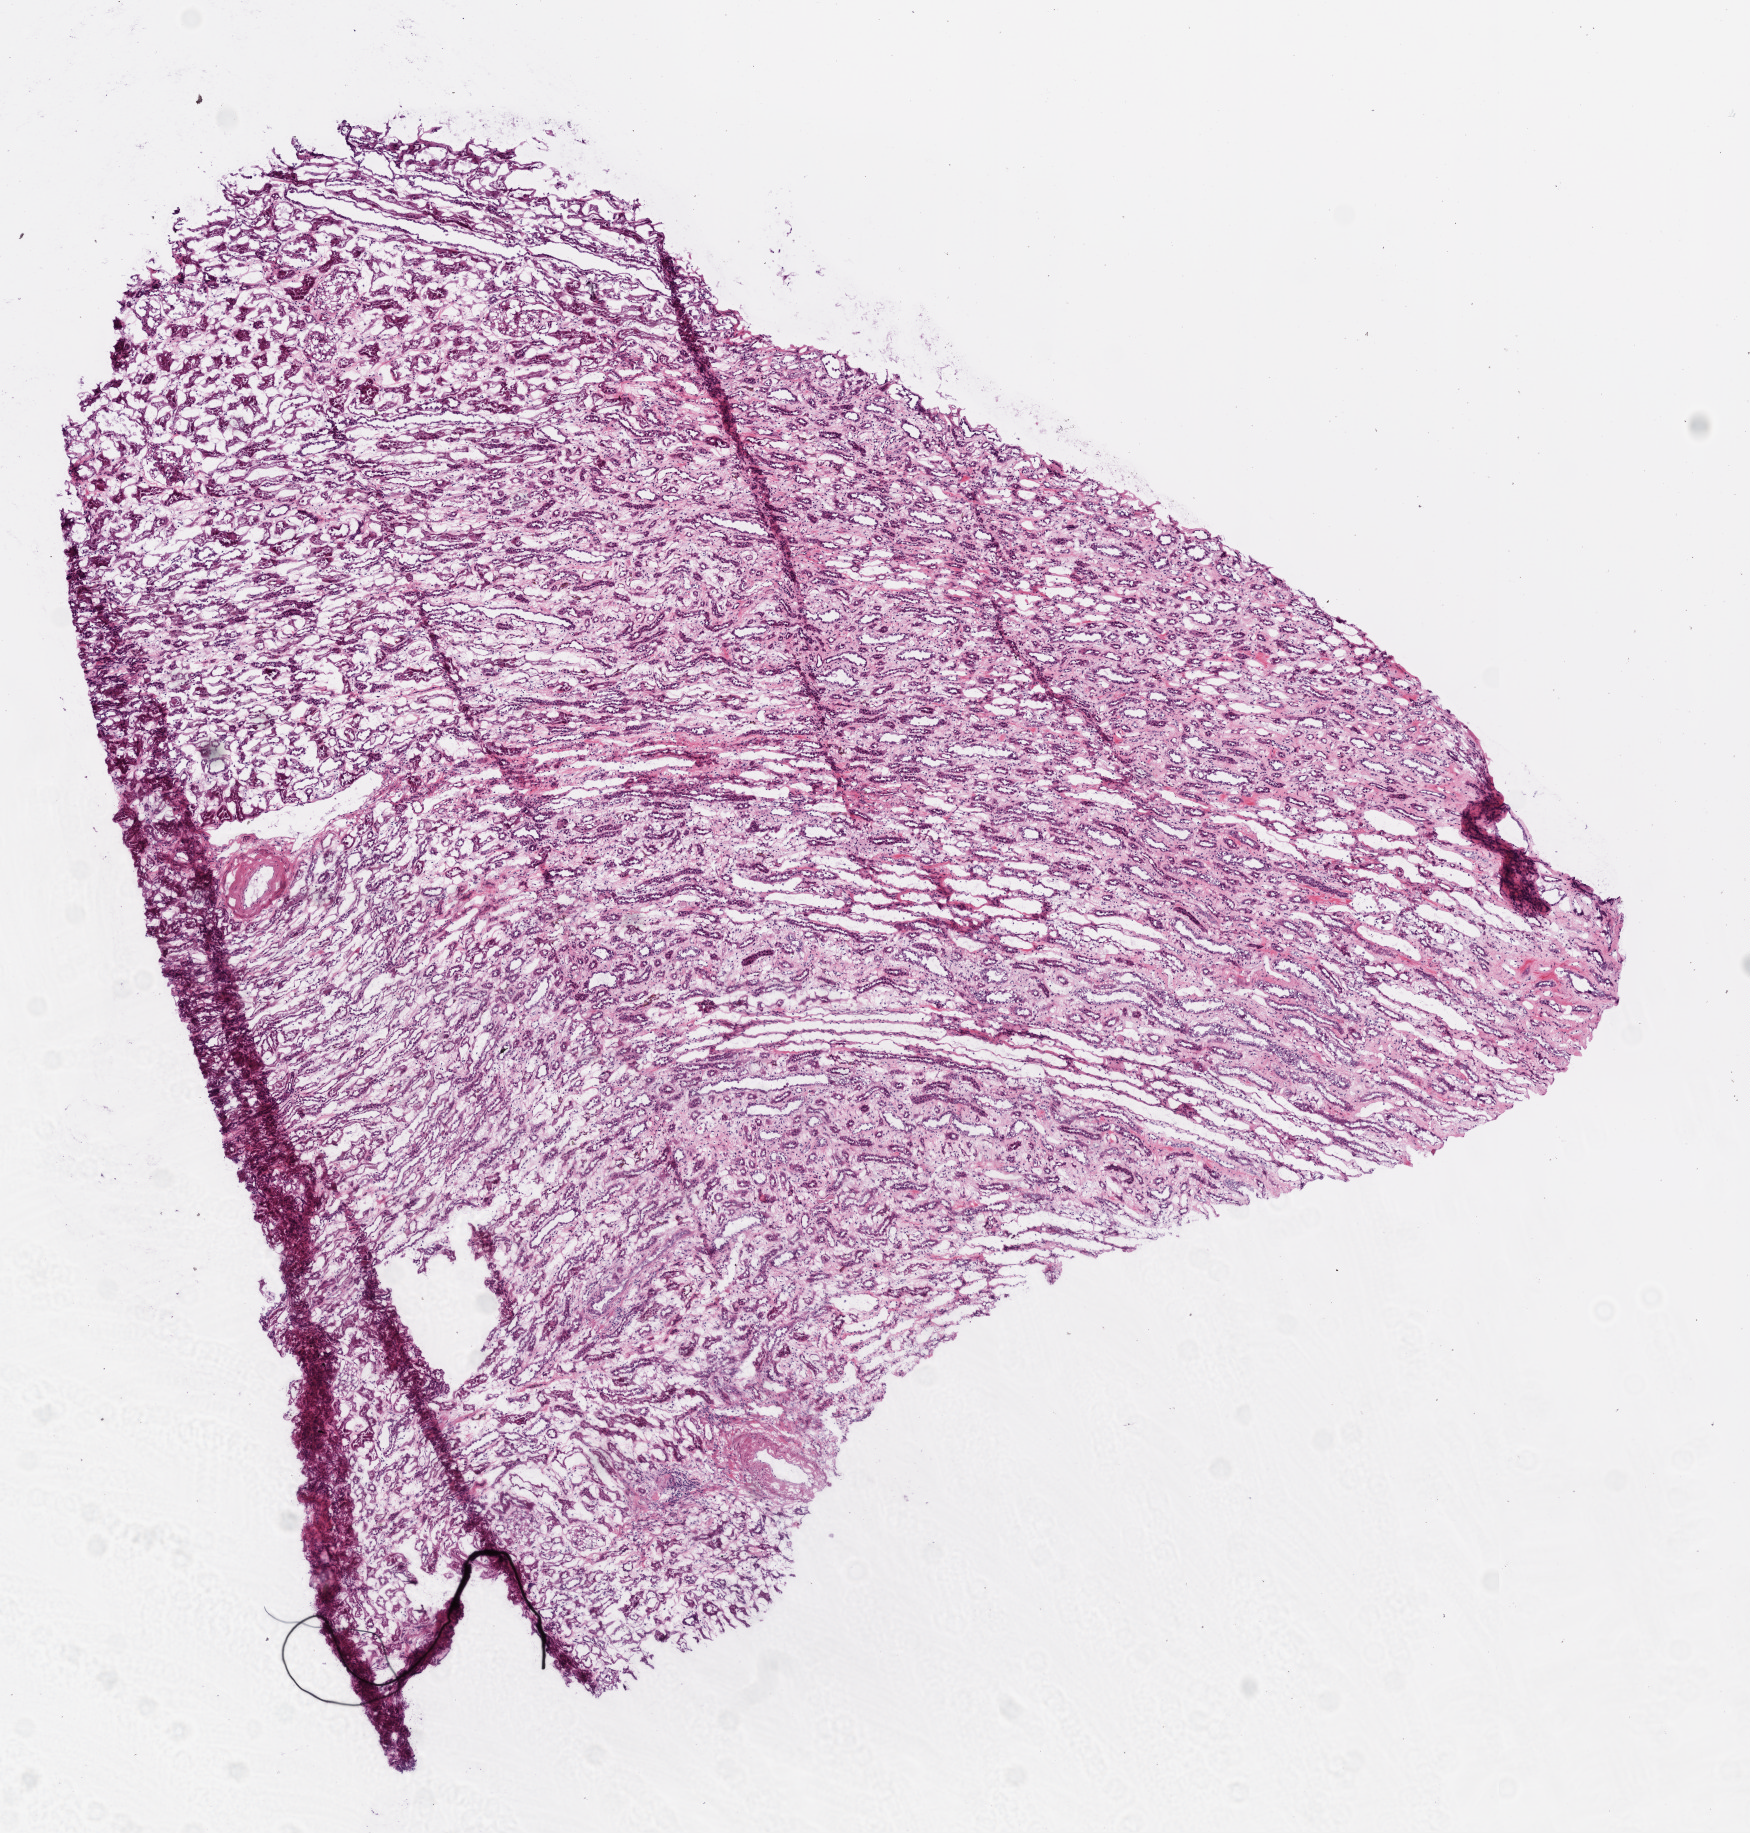
Digitized H&E-stained tissue section (whole slide) — whole scanned area (about 7.0 x 7.4 mm, from a 20x scan) shown as a low-resolution overview. Frozen section from the top of the tissue portion. Sample: solid tissue normal (non-tumour tissue), kidney. Female, age 76 years at initial diagnosis.
This section: solid tissue normal (non-tumour) sample from the same patient. Patient diagnosis: Clear cell adenocarcinoma, NOS.